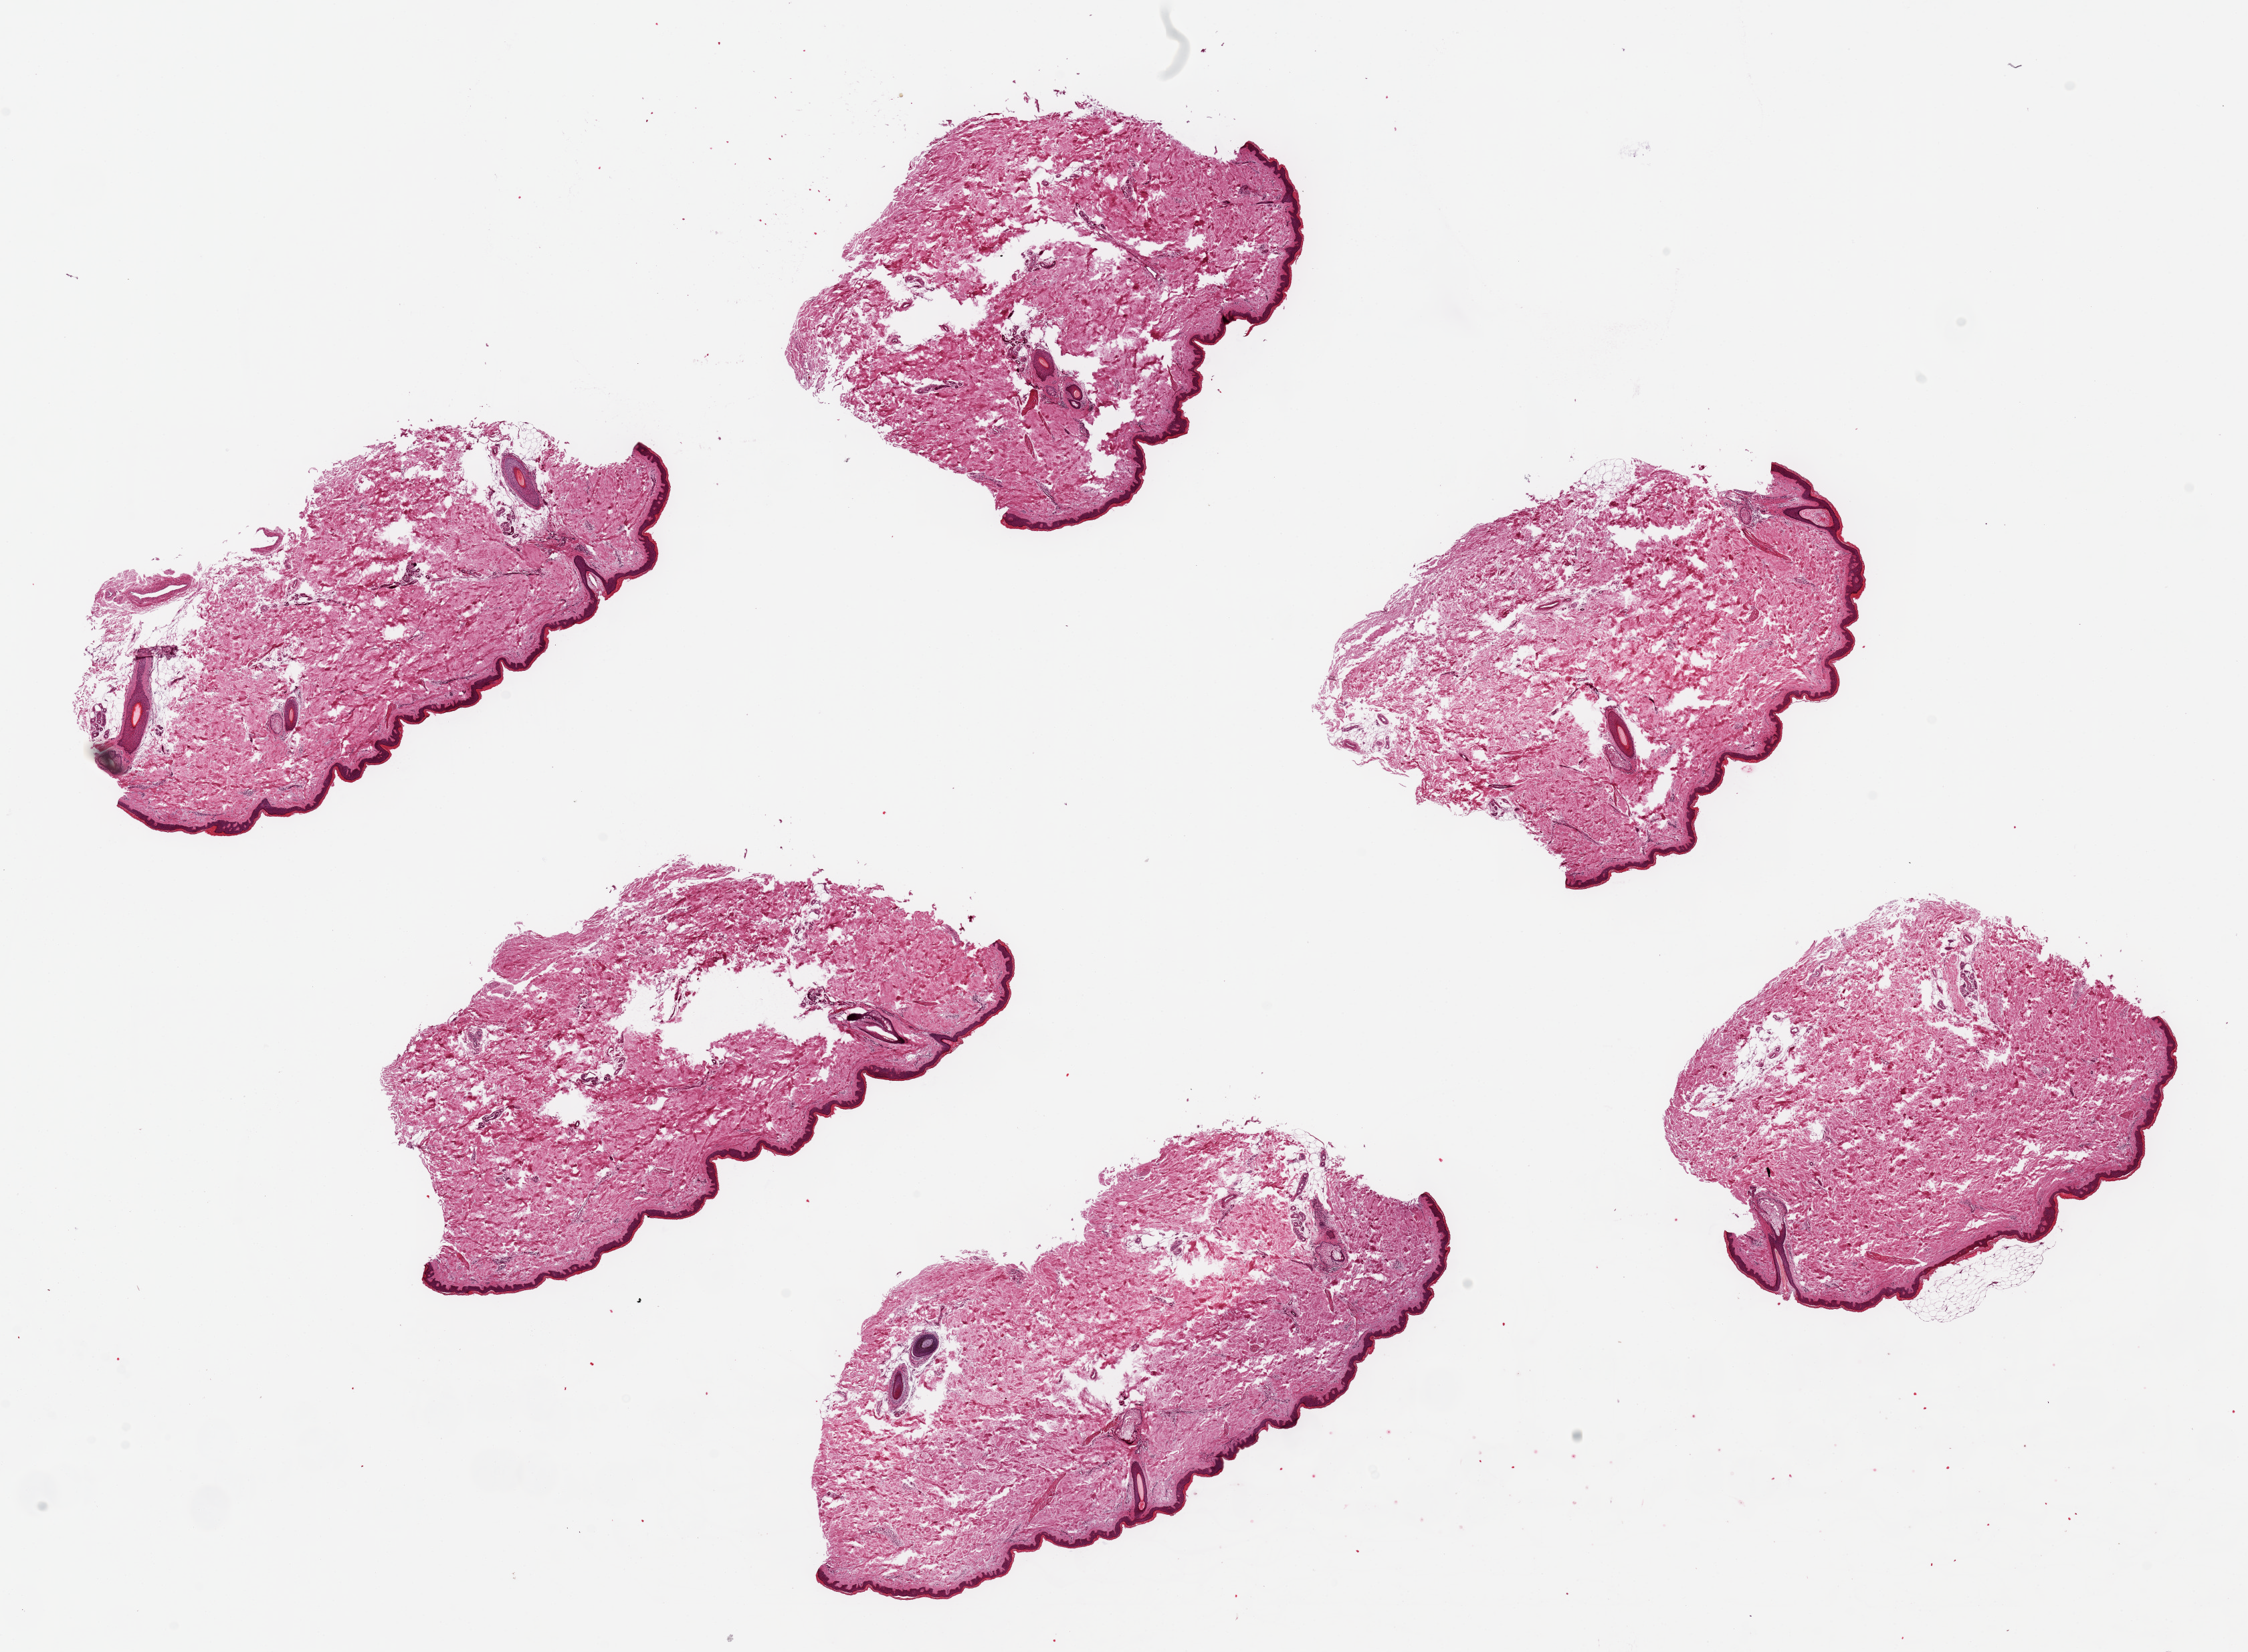
Haematoxylin and eosin whole-slide image, brightfield, whole scanned area (about 26.6 x 19.5 mm) shown as a low-resolution overview; PAXgene-fixed, paraffin-embedded tissue; sampled site (target tissue): skin of lower leg; donor tissue sample. Donor: male.
Pathologist's review note for this sample: 6 ~ 7x3.5 pieces; squamous mucosa is ~1.5???2% of thickness.